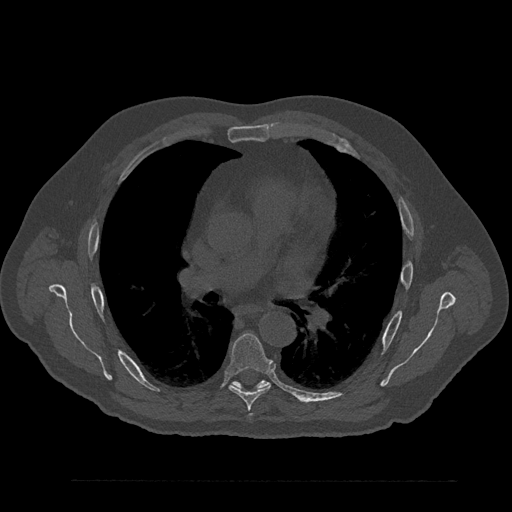
CT including the spine, one axial slice; slice 543 of 797 in the series (ordered by position); reconstruction kernel Br40s/3; bone window (W 1800 / L 400 HU); 0.5 mm slice thickness; 512 × 512 image matrix, field of view 430 × 430 mm. Male patient, age 61 years. From the clinical record (not read from this slice): primary cancer: prostate.
Outlined on this slice (semi-automatic segmentation, software-assisted and operator-edited):
- T6 vertebra: bounding box <227,333,273,421> (left, top, right, bottom; pixels)
- T7 vertebra: <234,380,269,389>